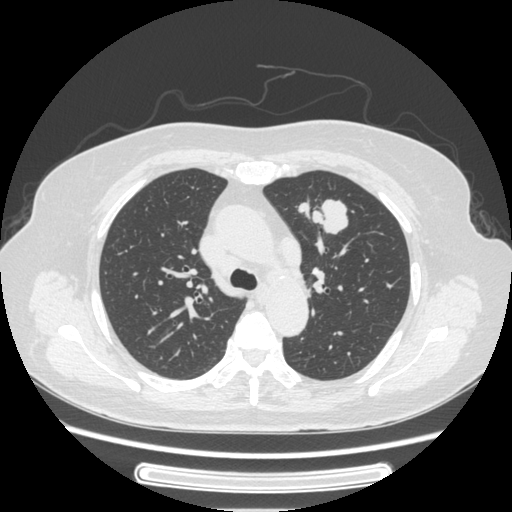
Chest CT, one axial slice; slice 167 of 227 in the series (ordered by position); reconstruction kernel STANDARD; lung window (W 1500 / L -600 HU); 1.25 mm slice thickness; 512 × 512 image matrix, field of view 363 × 363 mm. Patient: female, 77 years. From the clinical record (not read from this slice): clinical TNM (as recorded): T1c N3 M0.
Outlined on this slice (bounding box drawn by a radiologist):
- lung tumour (recorded histology: adenocarcinoma): bounding box [x1, y1, x2, y2] px = [295, 187, 354, 239]